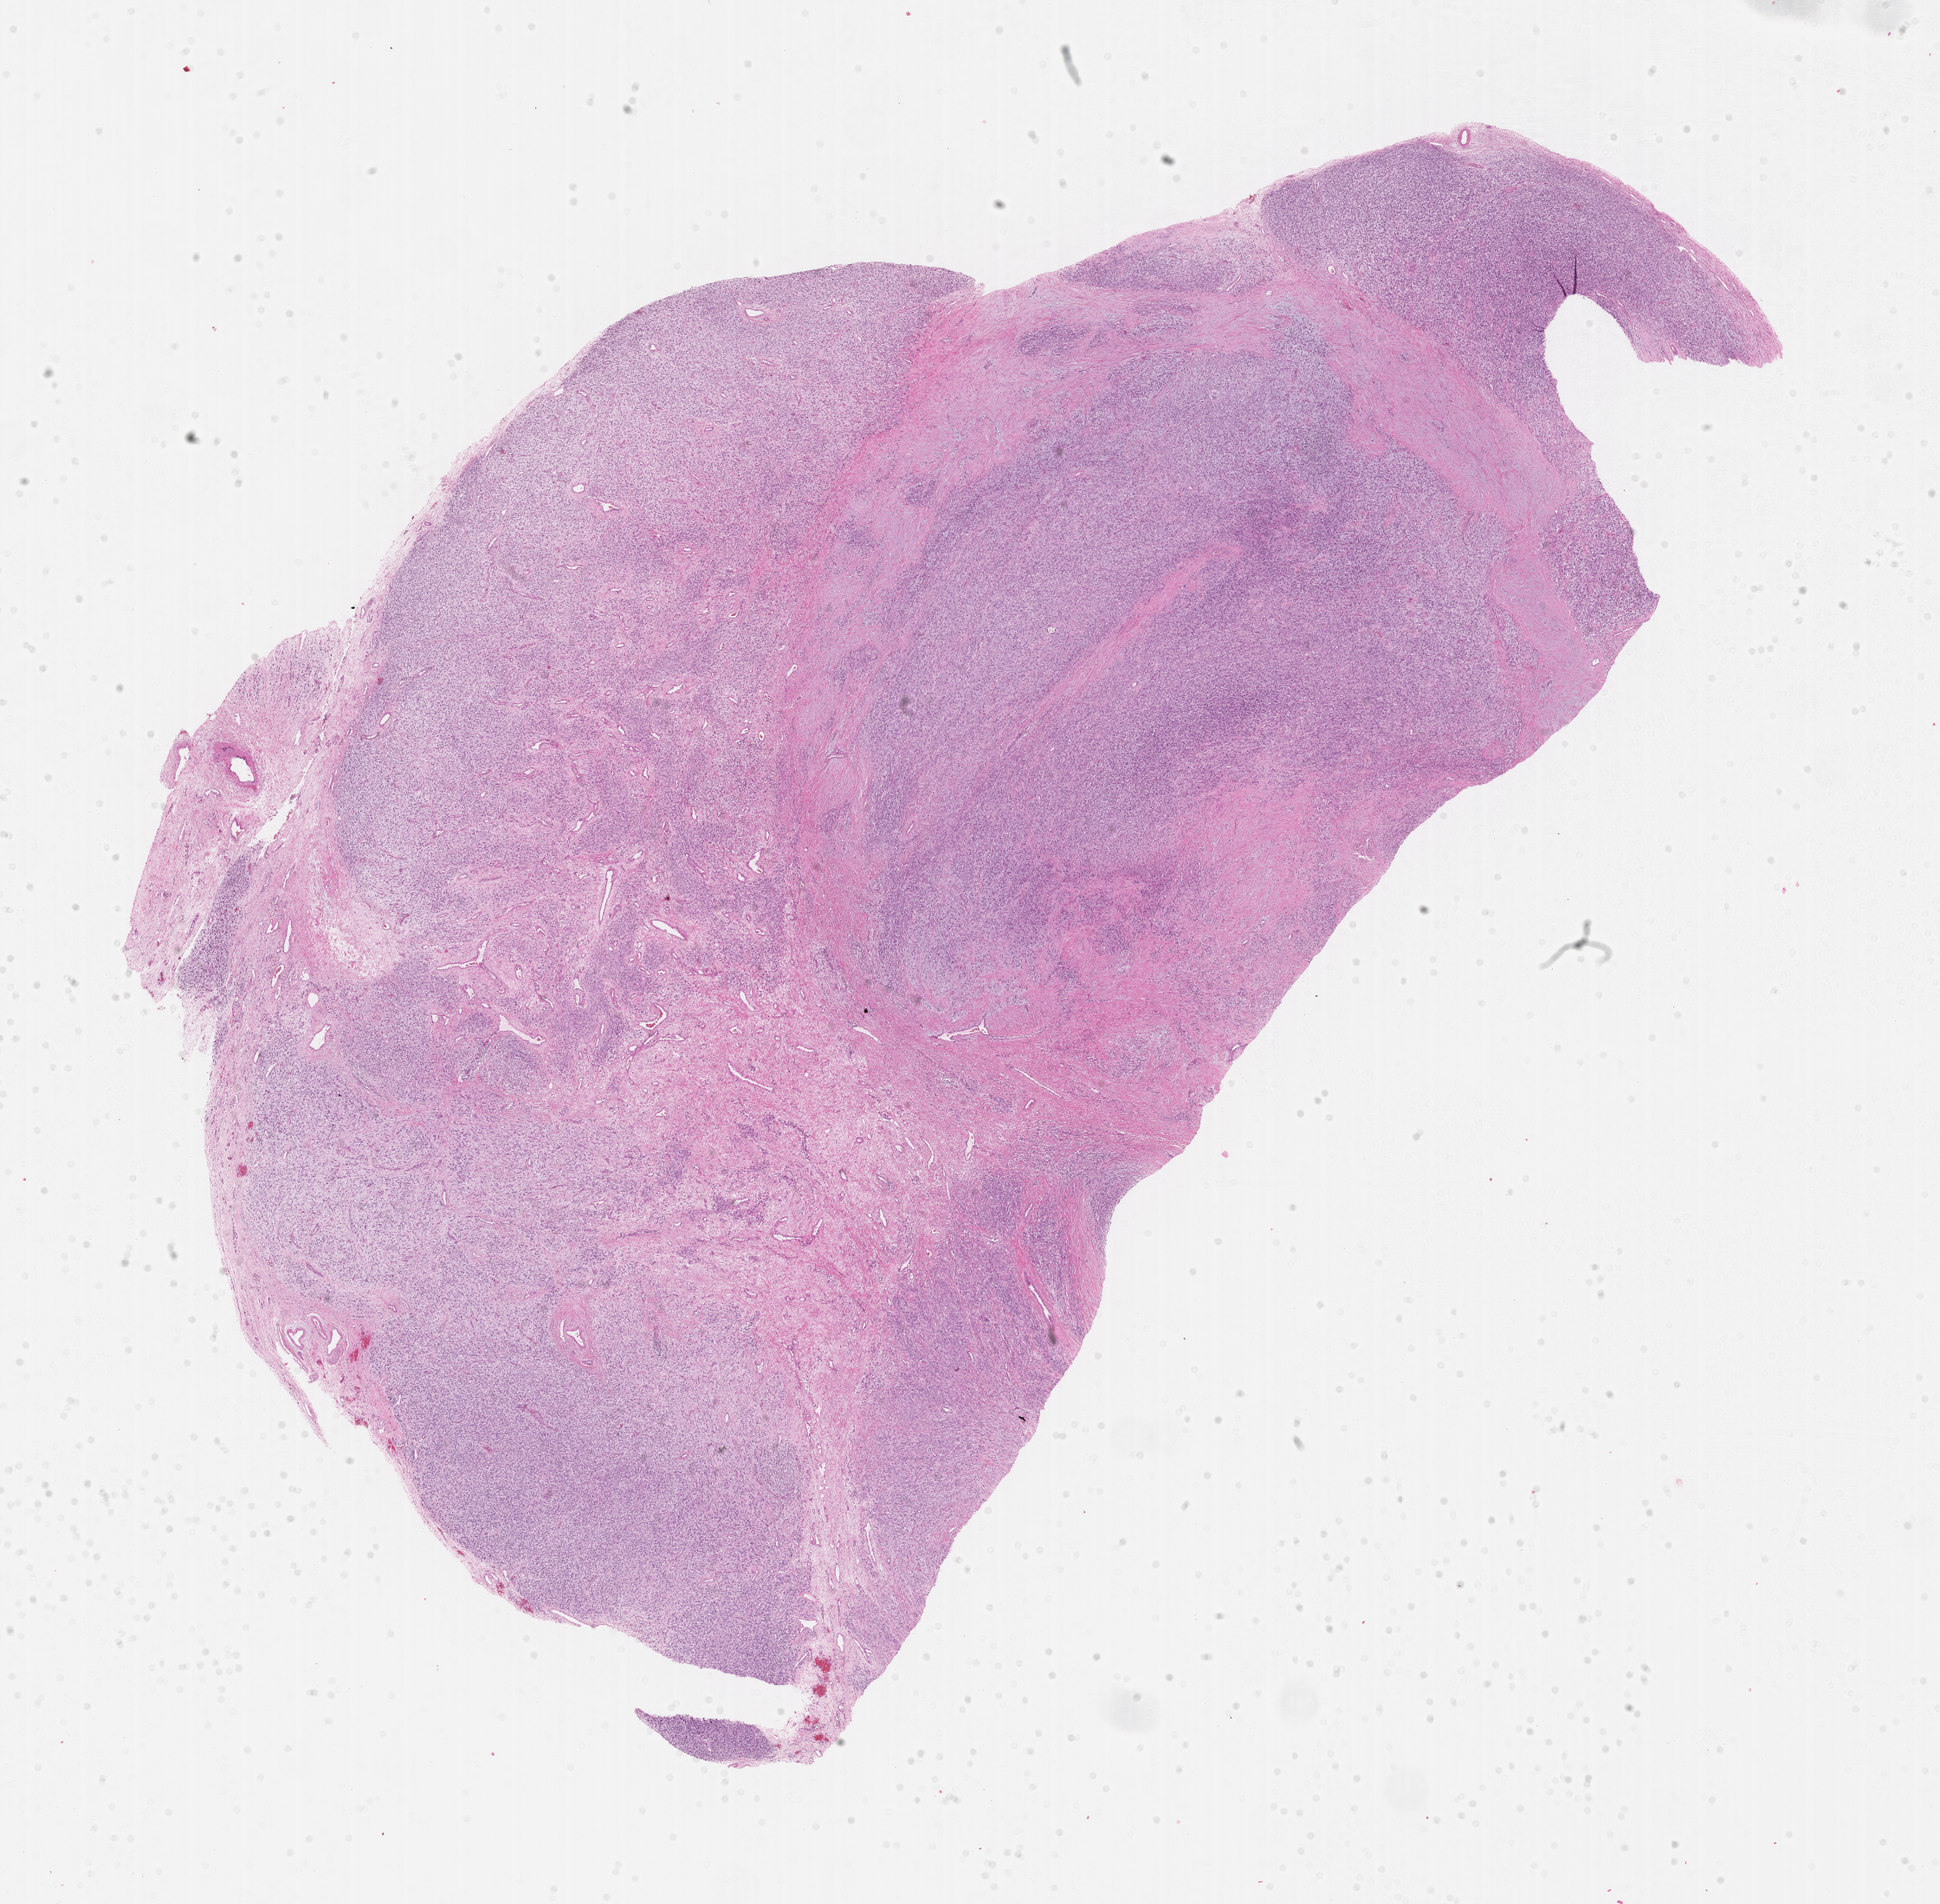
Hematoxylin and eosin (H&E) whole-slide image of tumor tissue — shown as a low-resolution overview of the whole scanned area (about 18.1 x 17.8 mm). FFPE section. Site: testicle, right. Male patient, age at diagnosis 4.1 years.
Stage (as recorded): 1. Diagnosis: rhabdomyosarcoma; histological classification: embryonal rhabdomyosarcoma.